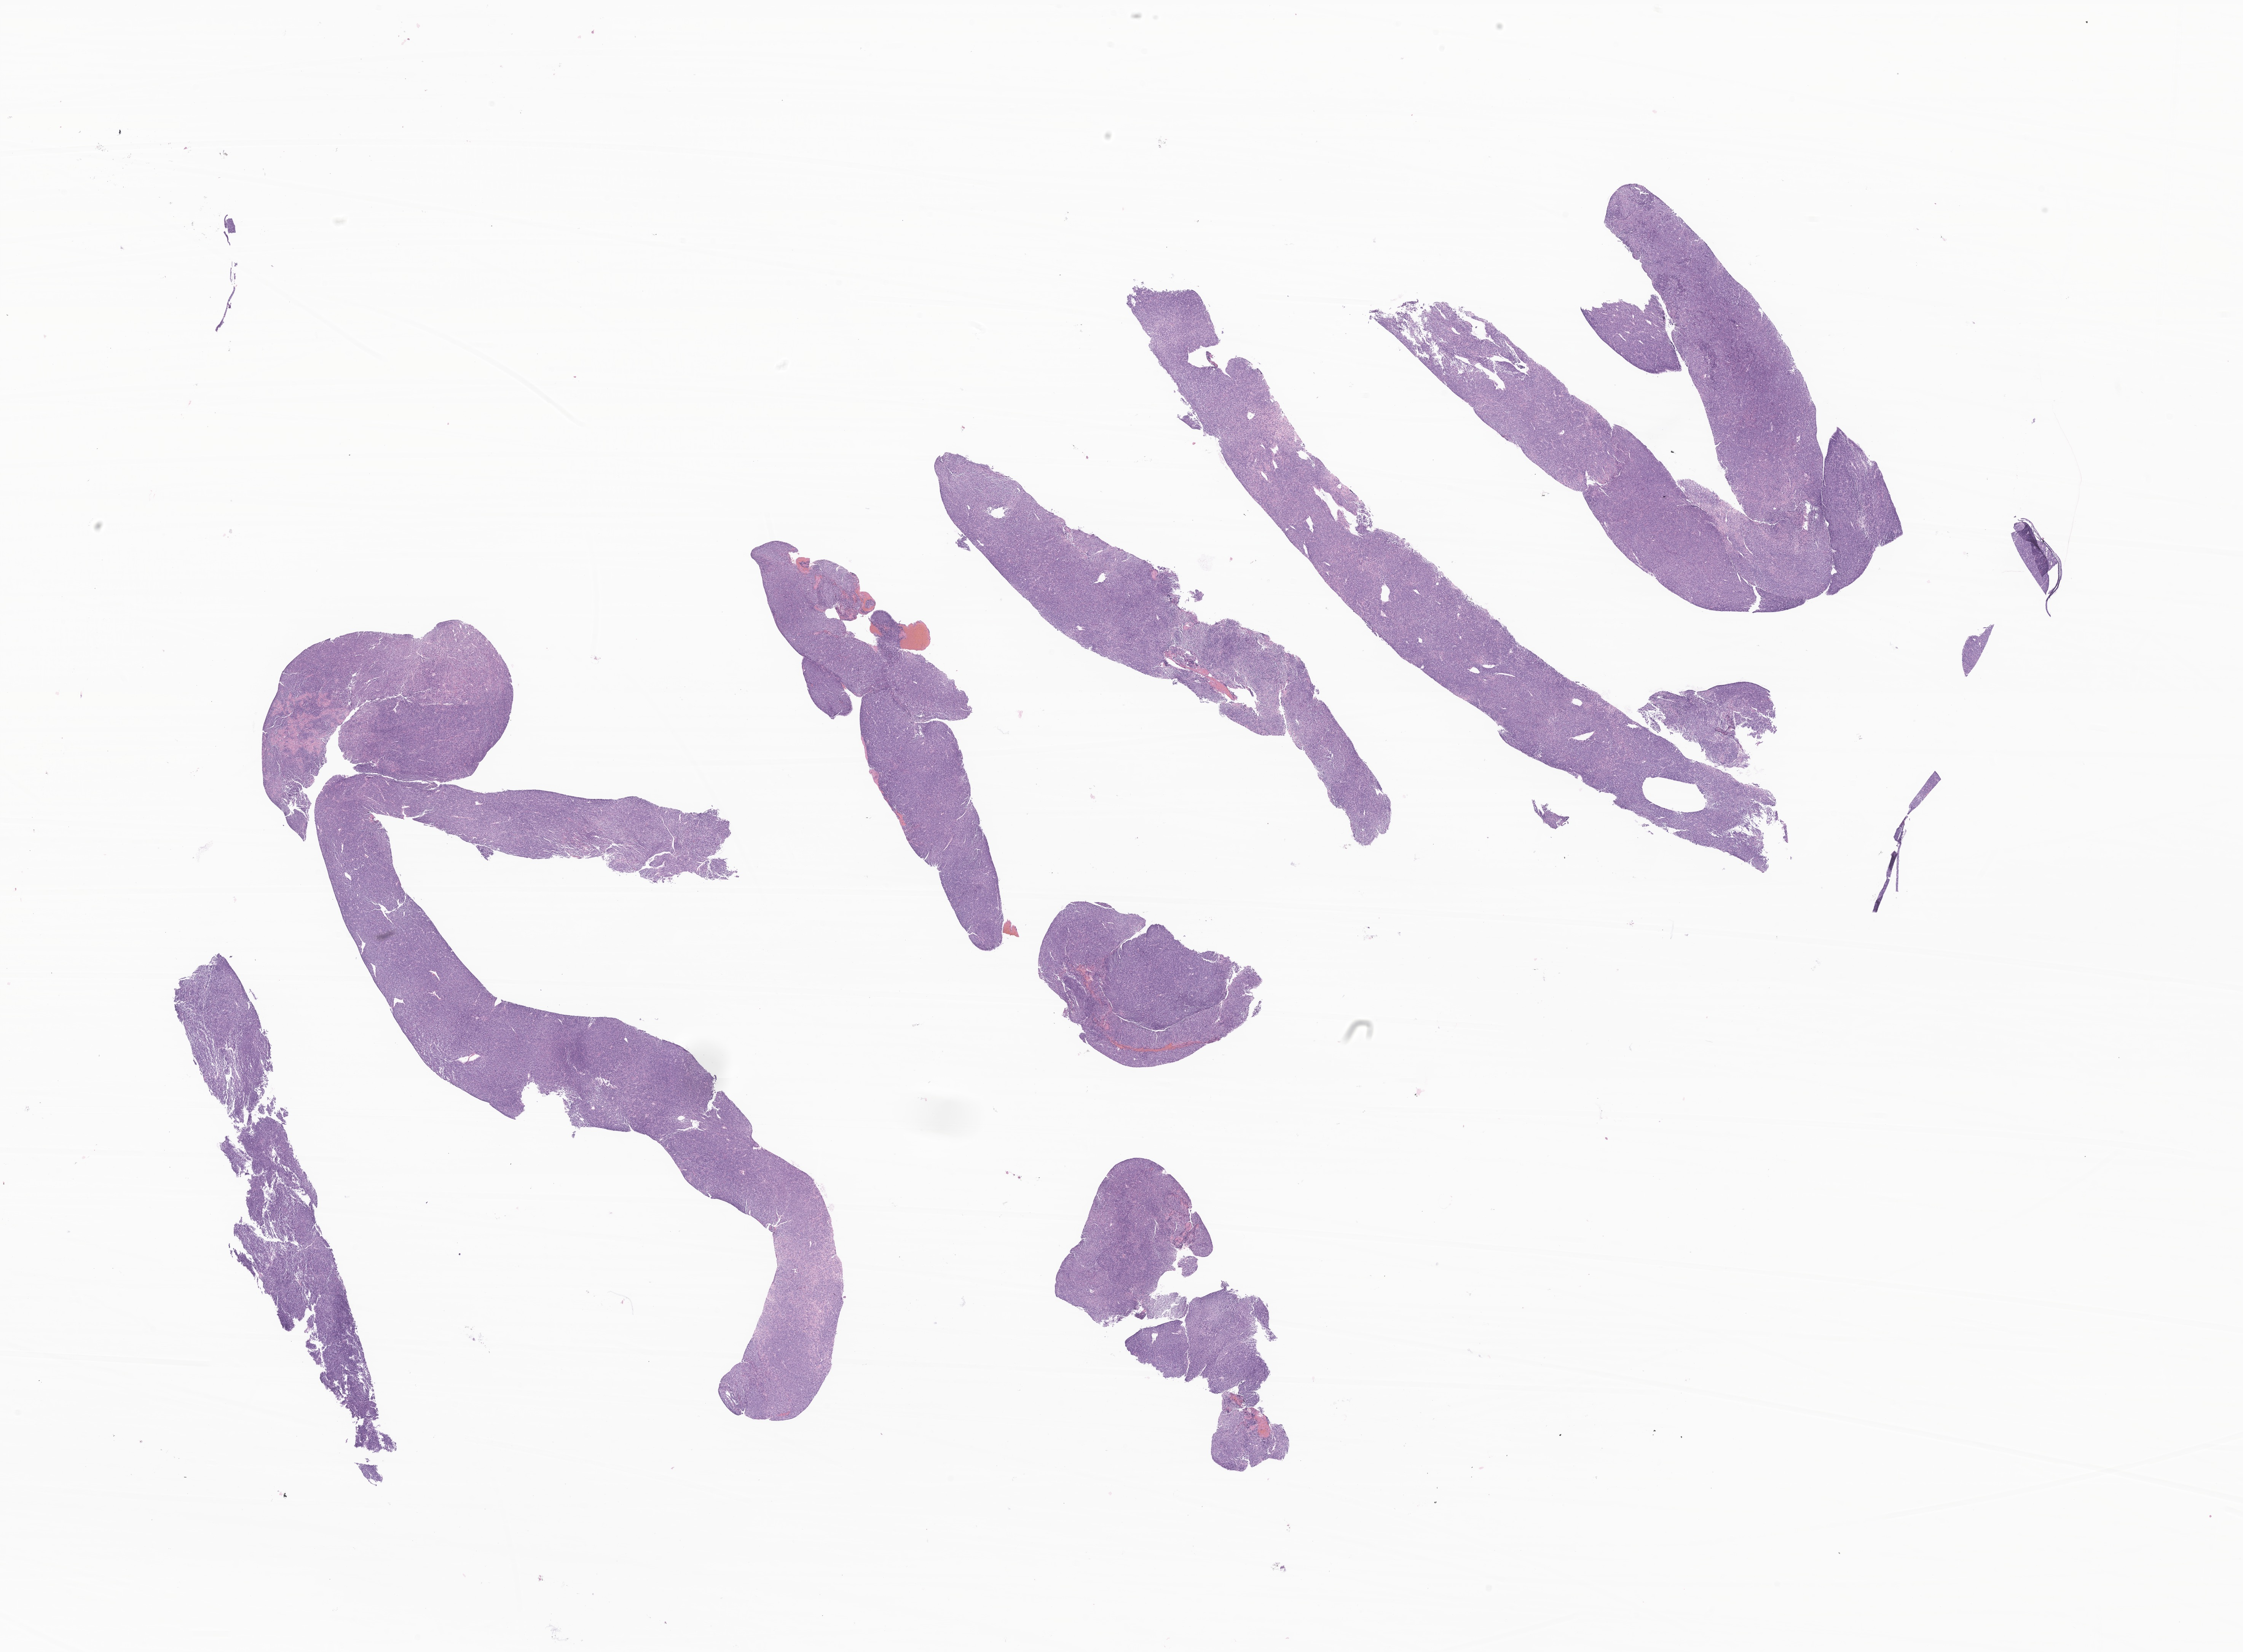
Digitized haematoxylin and eosin-stained section of tumor tissue — a low-resolution overview of the entire scanned area, about 24.8 x 18.3 mm, formalin-fixed, paraffin-embedded (FFPE) tissue. Female patient, age 187 months (15 years 7 months).
Recorded diagnosis: Synovial sarcoma, NOS.